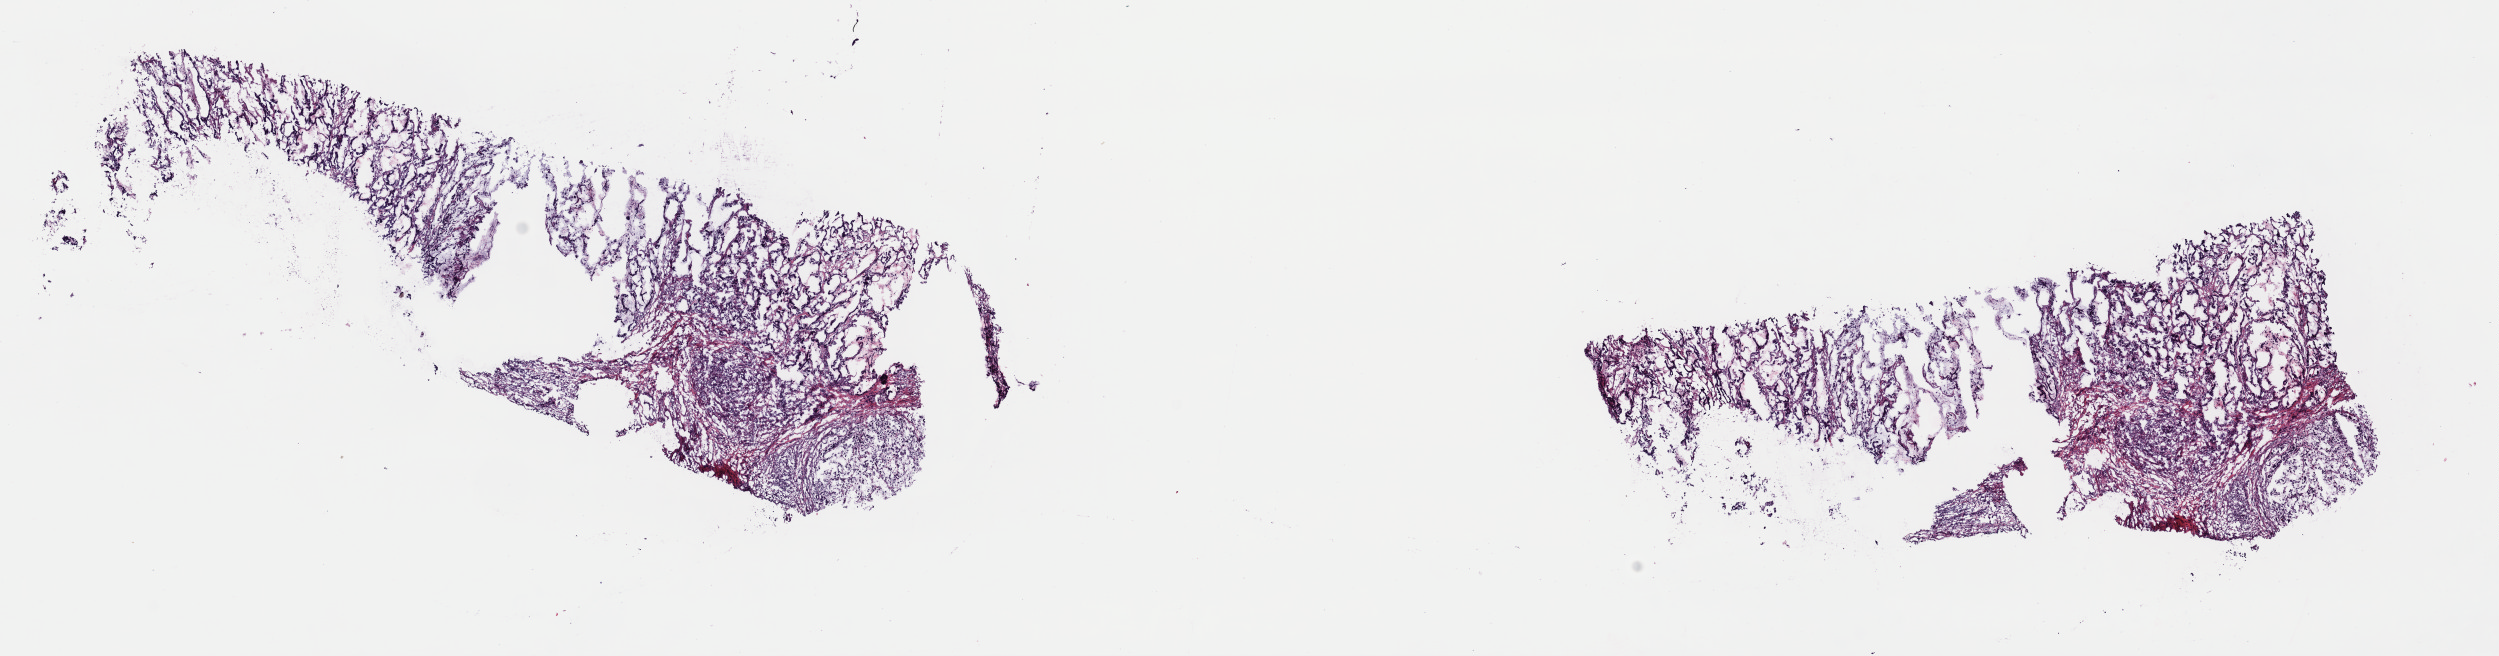
Whole-slide histology image, Hematoxylin and eosin (H&E) stained — low-resolution overview of the scanned area, about 19.7 x 5.2 mm. Frozen section from the top of the tissue portion. Stomach, primary tumour sample. Patient: male, age at initial diagnosis 76 years. Histologic grade: G3 (poorly differentiated). Pathologist review of this section (percent, as recorded): tumour cells 80%, tumour nuclei 80%, normal cells 0%, stromal cells 20%, necrosis 0%. Infiltration values recorded for this section: lymphocyte infiltration 0%, monocyte infiltration 0%, neutrophil infiltration 0%.
- histologic diagnosis: Carcinoma, diffuse type (cardia, NOS)
- AJCC pathologic stage: IIA